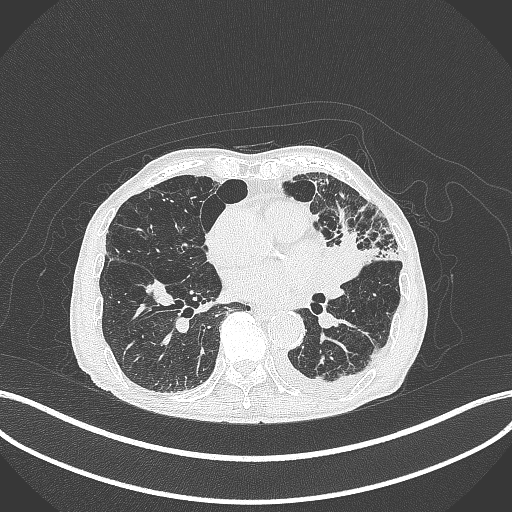
Chest CT, one axial slice; slice 169 of 385 in the series (ordered by position); 120 kVp; lung window (W 1500 / L -600 HU); 512 × 512 image matrix. Patient: male, 90 years or older. Case-level facts recorded for this patient, not image findings: clinical TNM (as recorded): T2b N1 M0.
Structures marked on this image (rectangle marked by the reading radiologist):
- lung tumour (recorded histology: squamous cell carcinoma): bounding box [x1, y1, x2, y2] px = [323, 236, 376, 281]